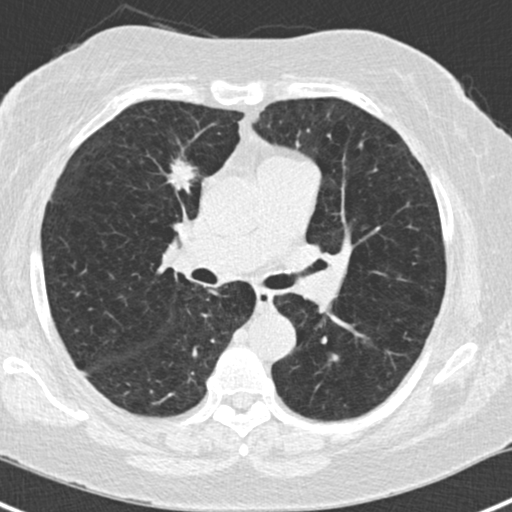
Low-dose screening chest CT, one axial slice. Position 88 of 168 along the scan axis. Reconstruction kernel B30f. Lung window (W 1500 / L -600 HU). 2 mm slice thickness. 512 × 512 image matrix, field of view 303 × 303 mm.
Annotated regions visible in this slice (outlined manually by an expert reader):
- lesion 1 (tumor, upper lobe of right lung): bounding box <168,159,195,193> (left, top, right, bottom; pixels)